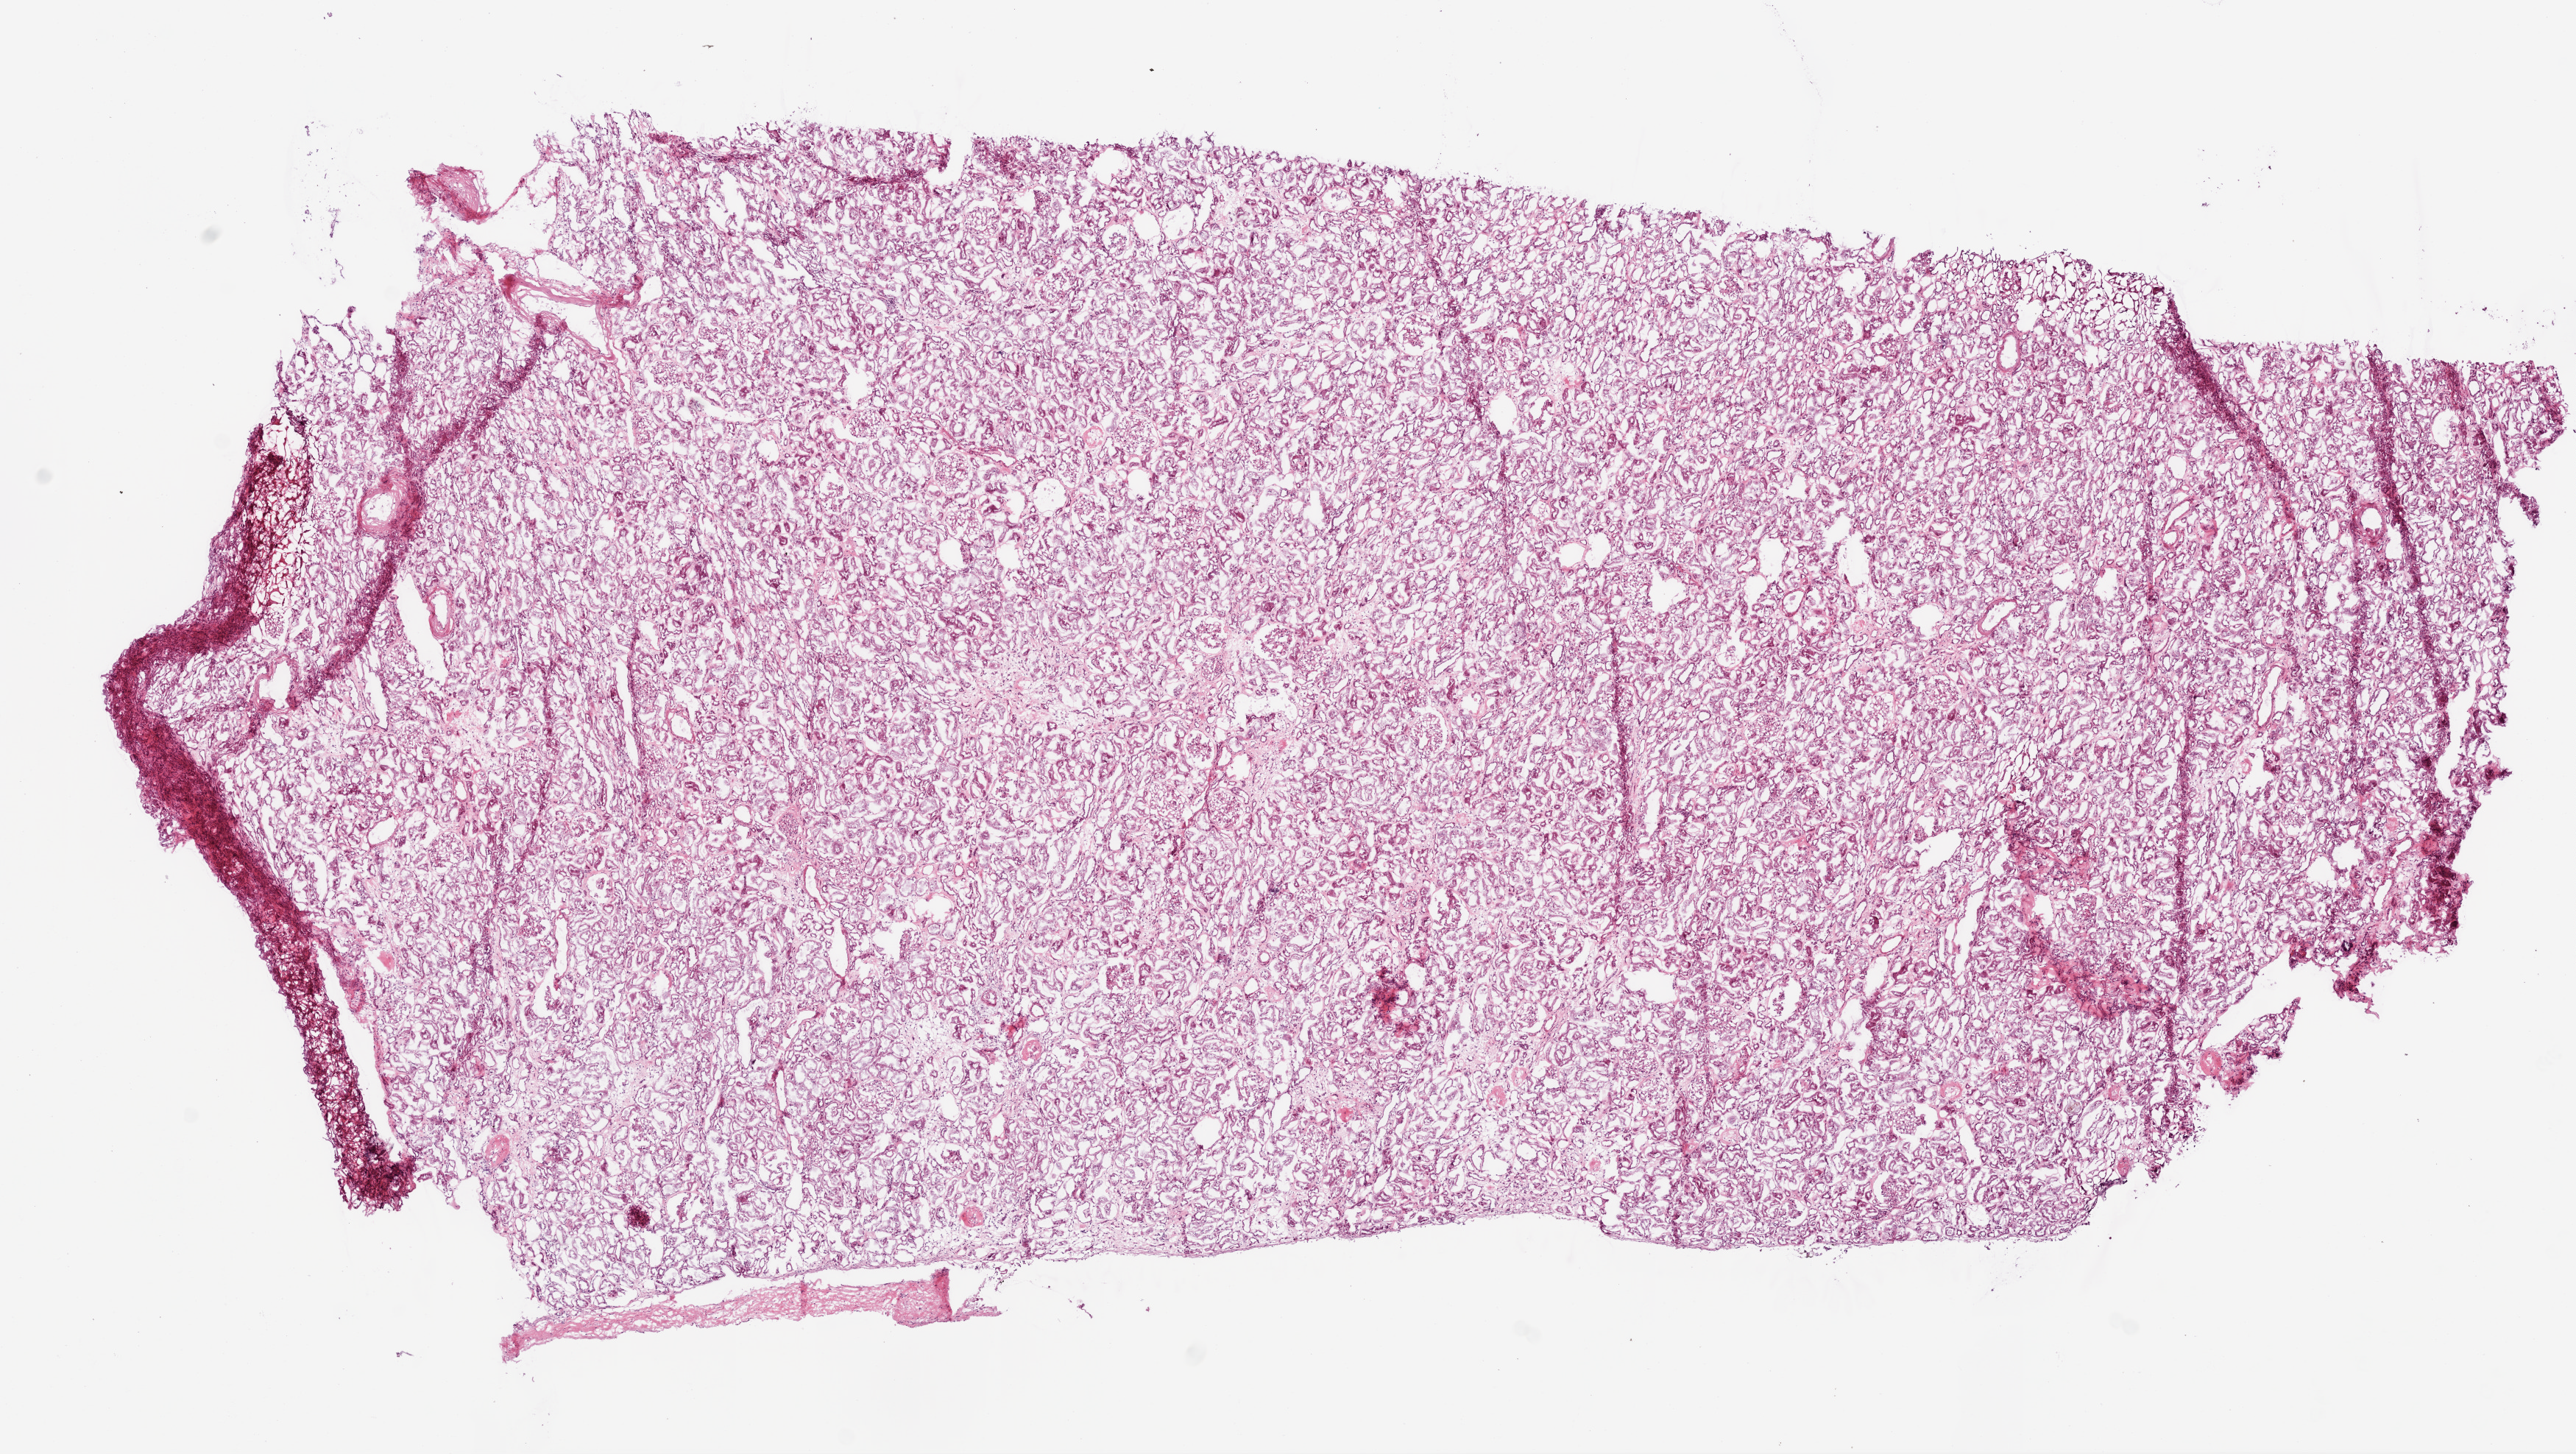
Whole-slide histology image, Hematoxylin and eosin (H&E) stained — whole scanned area (about 14.0 x 7.9 mm, slide scanned at 20x) shown as a low-resolution overview, frozen section from the top of the tissue portion, sample: solid tissue normal (non-tumour tissue), kidney. Female patient.
This section: solid tissue normal sample (biorepository sample class). Patient diagnosis: Clear cell adenocarcinoma, NOS.